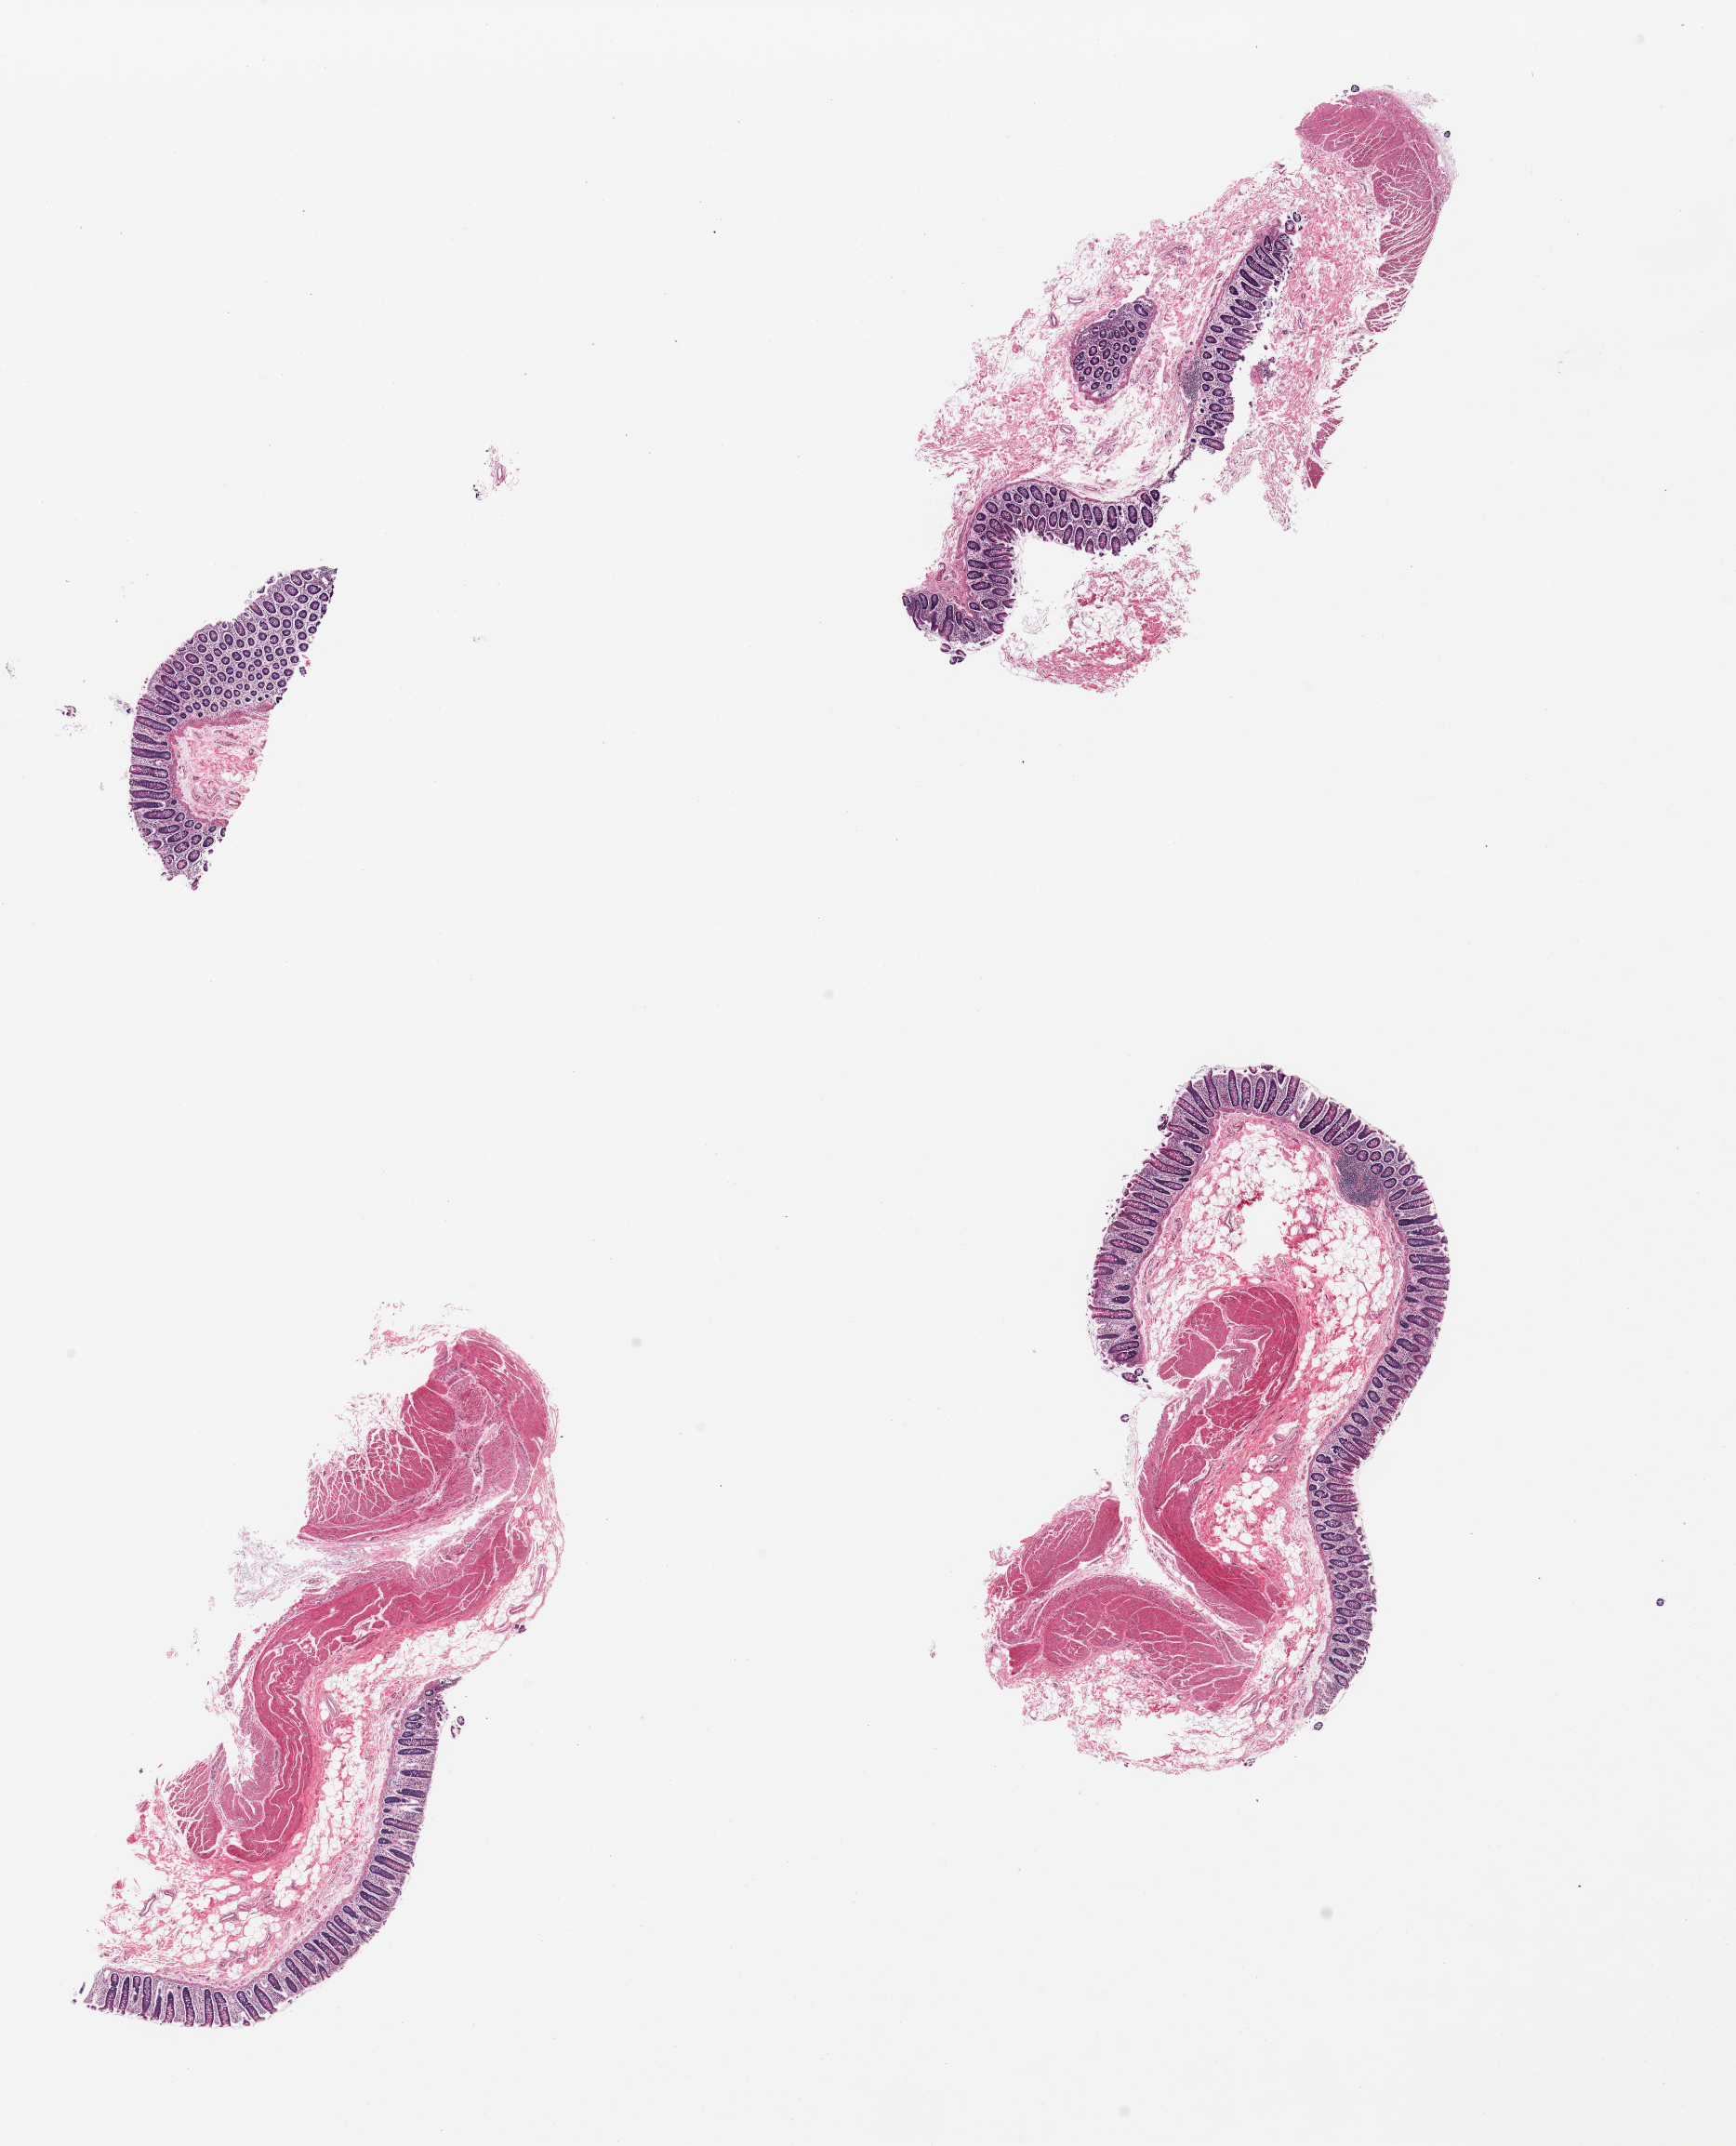
Haematoxylin and eosin whole-slide image, low-resolution overview of the scanned area, about 14.8 x 18.3 mm, PAXgene-fixed, paraffin-embedded tissue, target tissue: transverse colon, tissue donor sample. Male donor.
• pathologist's review note for this sample: 4 pieces; 1 has mucosa only